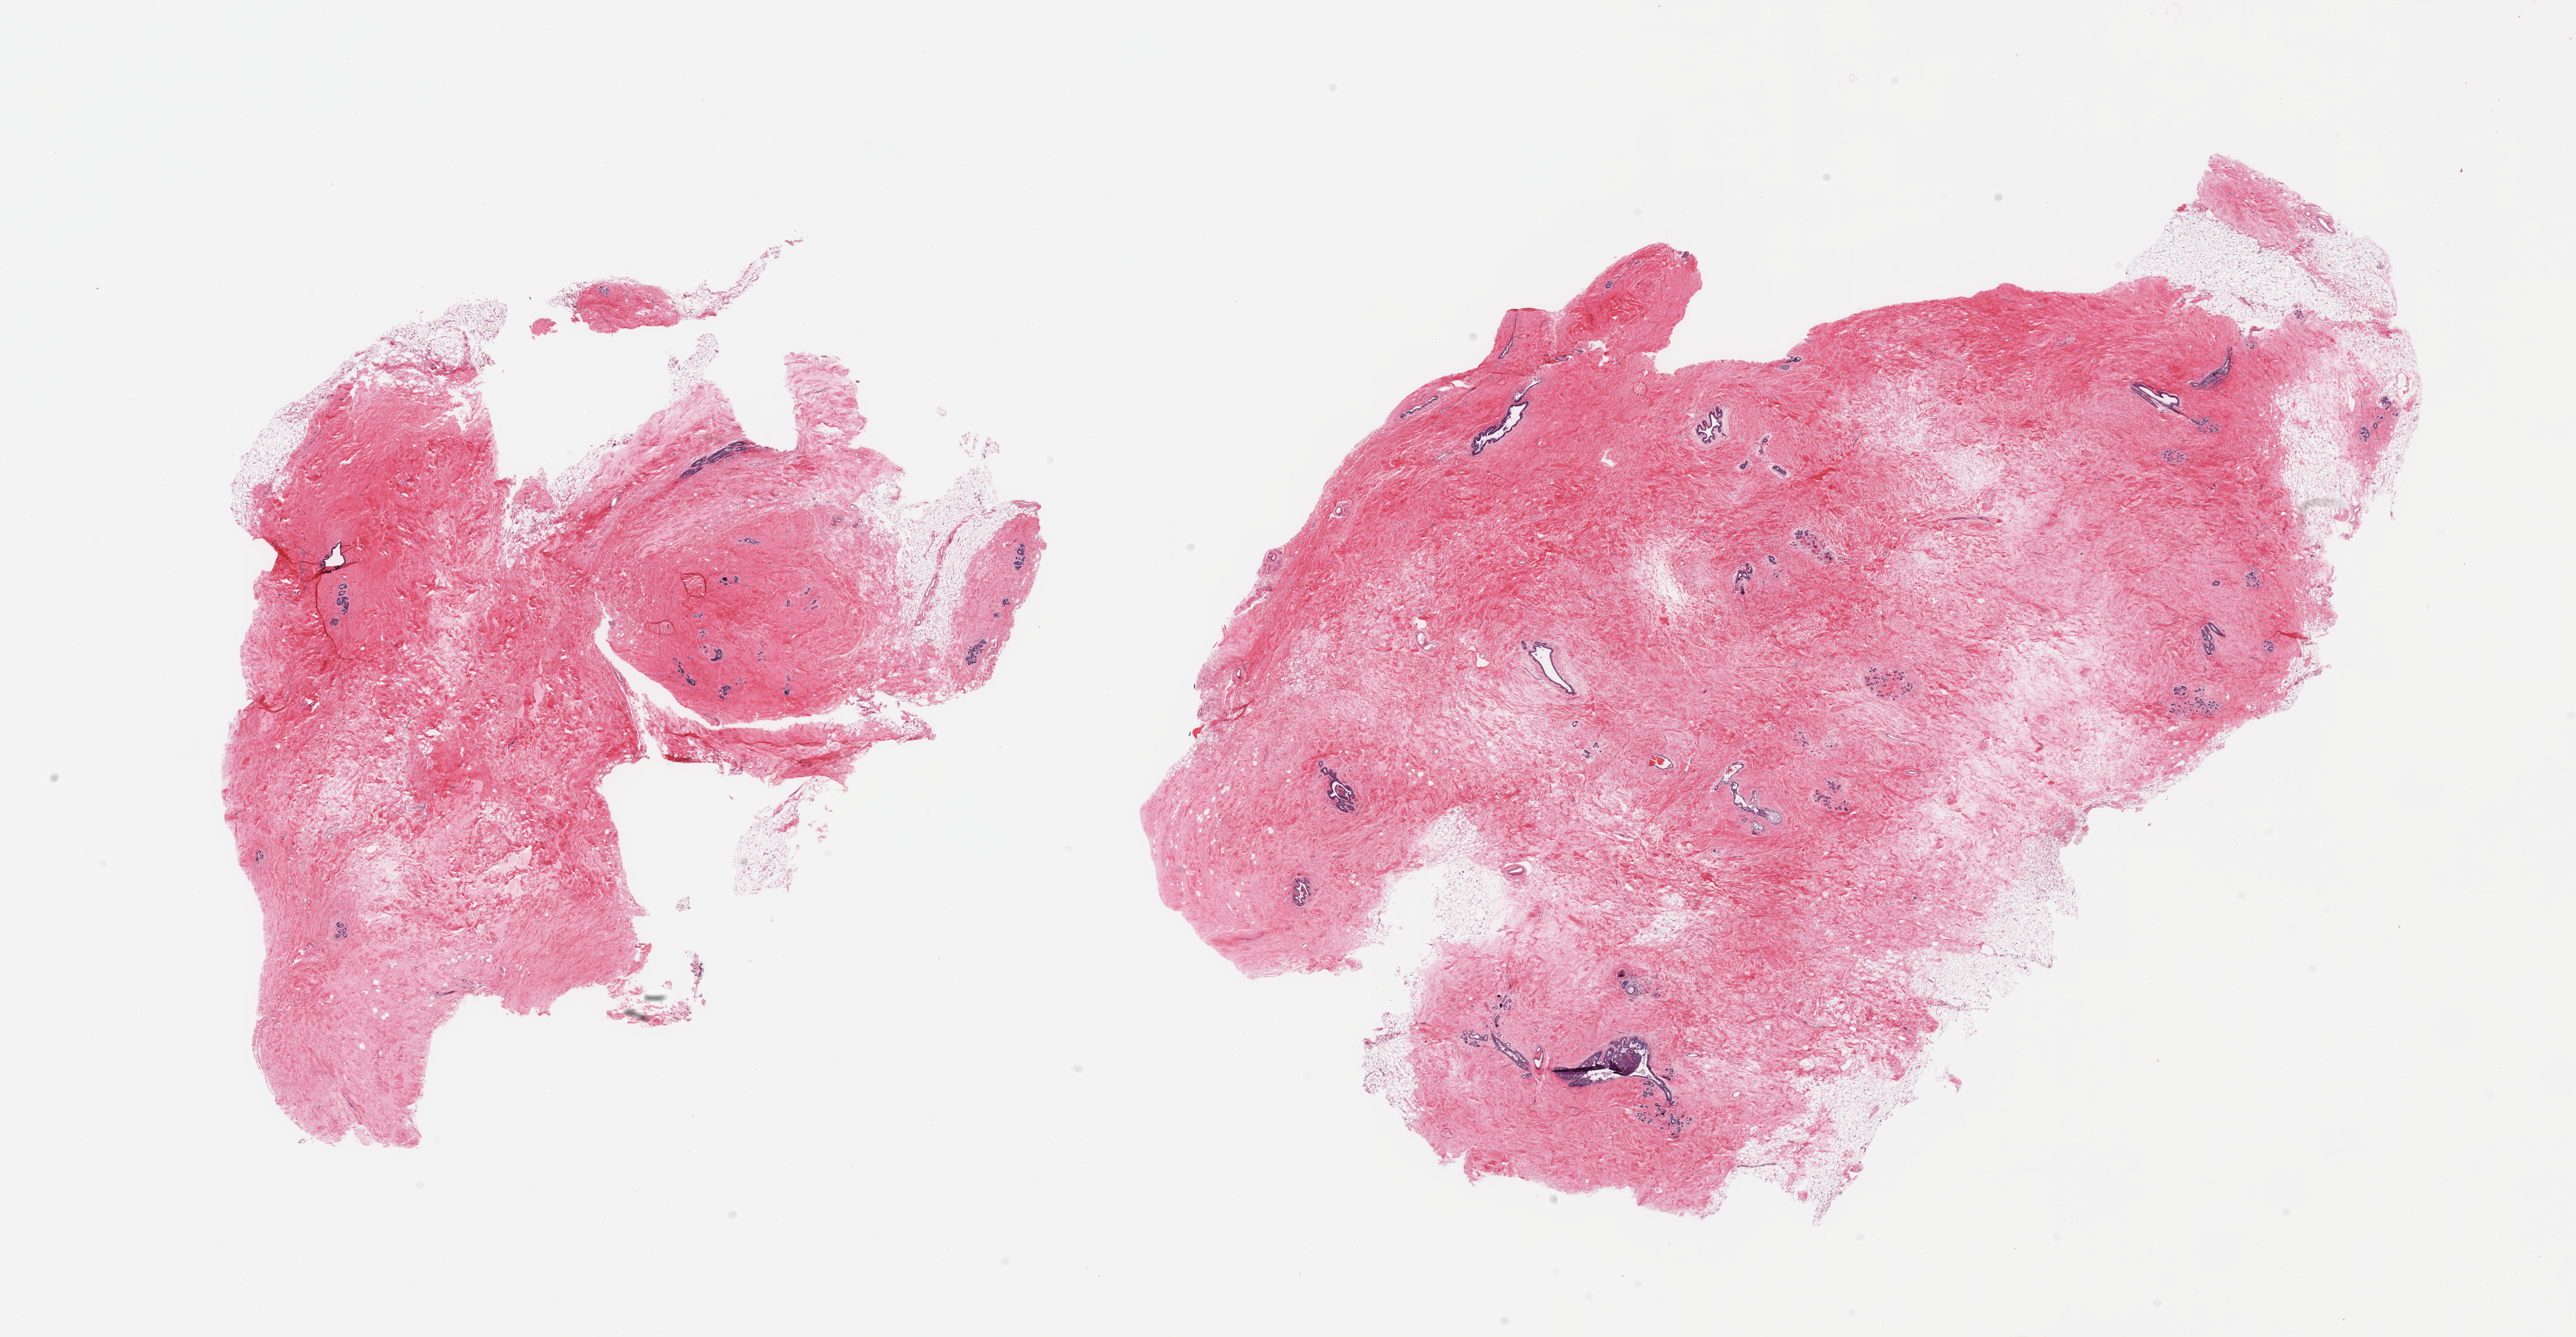
Digitized hematoxylin and eosin (H&E)-stained section — low-resolution overview of the scanned area, about 31.5 x 16.4 mm, PAXgene-fixed, paraffin-embedded tissue, sampled site (target tissue): breast, donor tissue sample. Donor: female.
Review note (as recorded): 2 pieces; atrophic ducts and lobules in fibrous stroma.